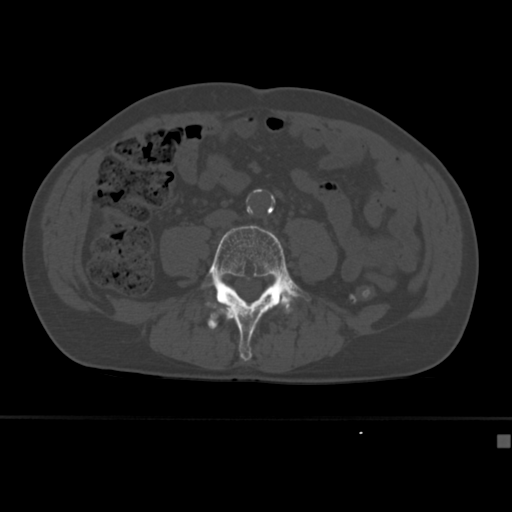
CT including the spine, one axial slice. Slice 105 of 430 in the series (ordered by position). Bone window (W 1800 / L 400 HU). 1.5 mm slice thickness. 512 × 512 image matrix, field of view 337 × 337 mm. Patient: male, 64 years. Case-level facts recorded for this patient, not image findings: primary cancer: uterus.
Structures marked on this image (semi-automatic segmentation, software-assisted and operator-edited):
- L4 vertebra: box from (x=199, y=225) to (x=312, y=362) px
- L5 vertebra: (x=291, y=298)–(x=295, y=302)